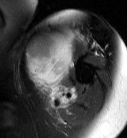
MRI of an extremity soft-tissue mass, one axial slice; slice 55 of 87 in the series (ordered by position); T2-weighted fat-saturated; MR volume resampled by the dataset authors to the PET/CT grid (not the native acquisition matrix); 3.27 mm slice thickness; 127 × 138 image matrix, field of view 124 × 135 mm. Female patient. Case-level facts recorded for this patient, not image findings: histological type: pleiomorphic leiomyosarcoma; grade: high; site of the primary tumour: left biceps.
Annotated regions visible in this slice (expert contour drawn on MRI and transferred to this co-registered scan by the dataset authors):
- gross tumour volume including surrounding oedema: bounding box <27,30,76,104> (left, top, right, bottom; pixels)
- gross tumour volume (mass): <25,30,75,88>